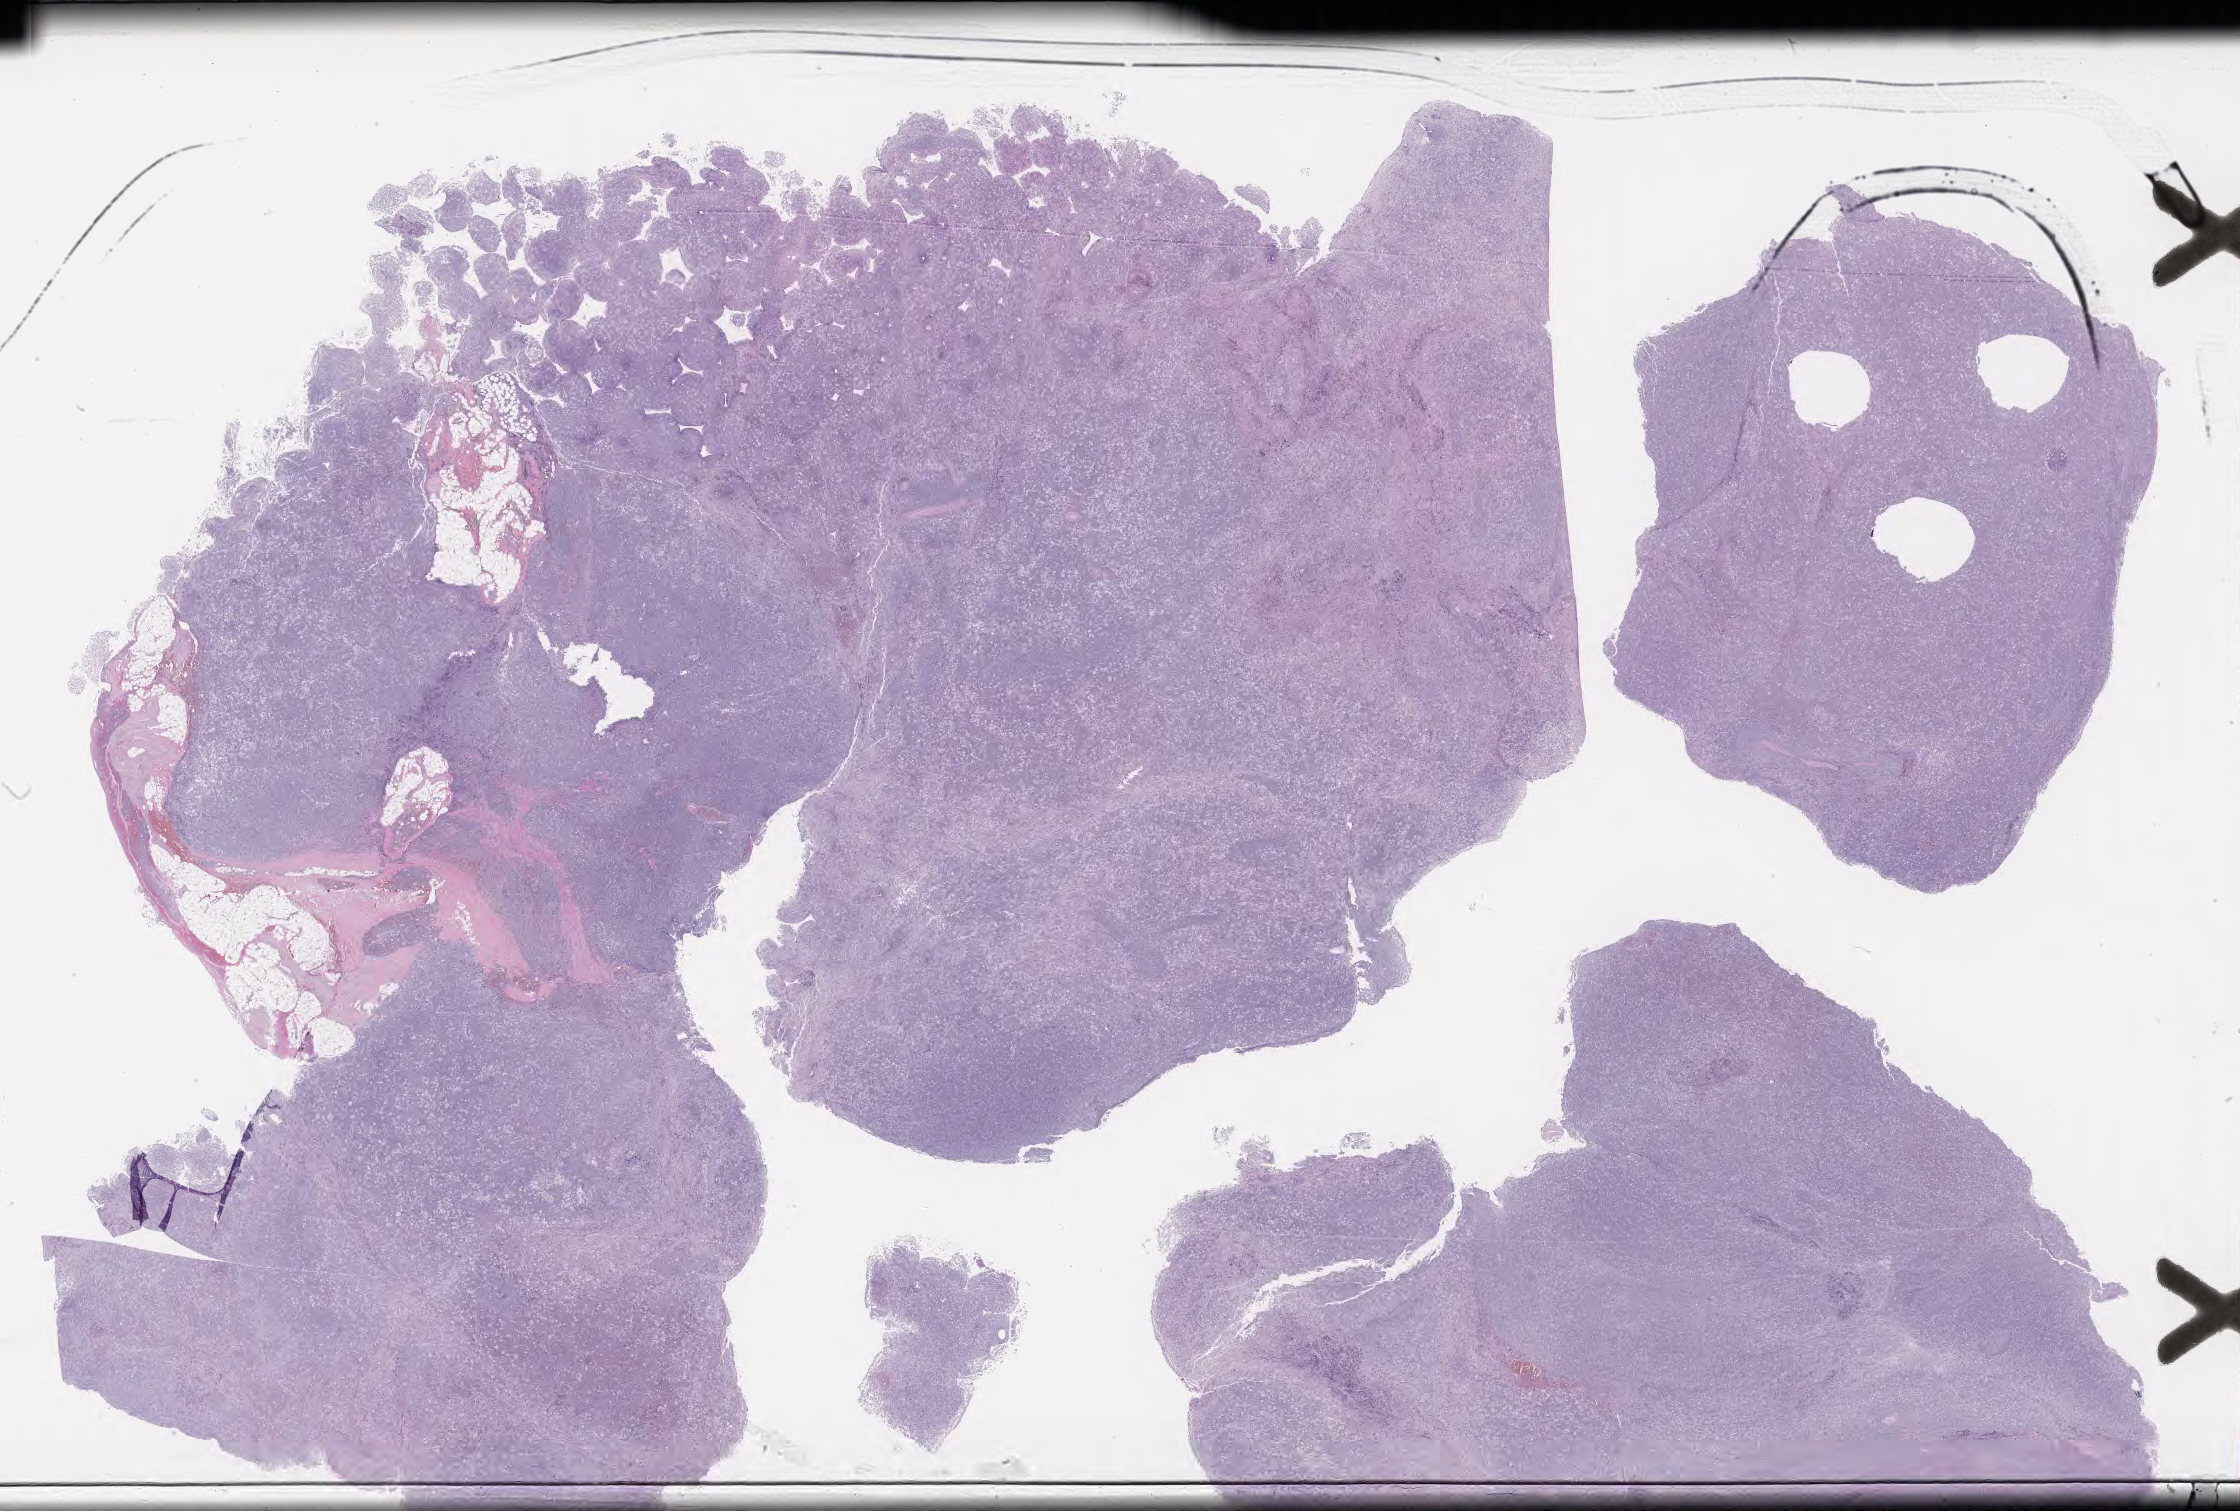
H&E whole-slide image, whole scanned area (about 36.2 x 24.4 mm) shown as a low-resolution overview, specimen: tumor tissue, site: lymph node of head and neck. Patient: male, 51 years old.
Histologic diagnosis: Burkitt lymphoma, NOS.